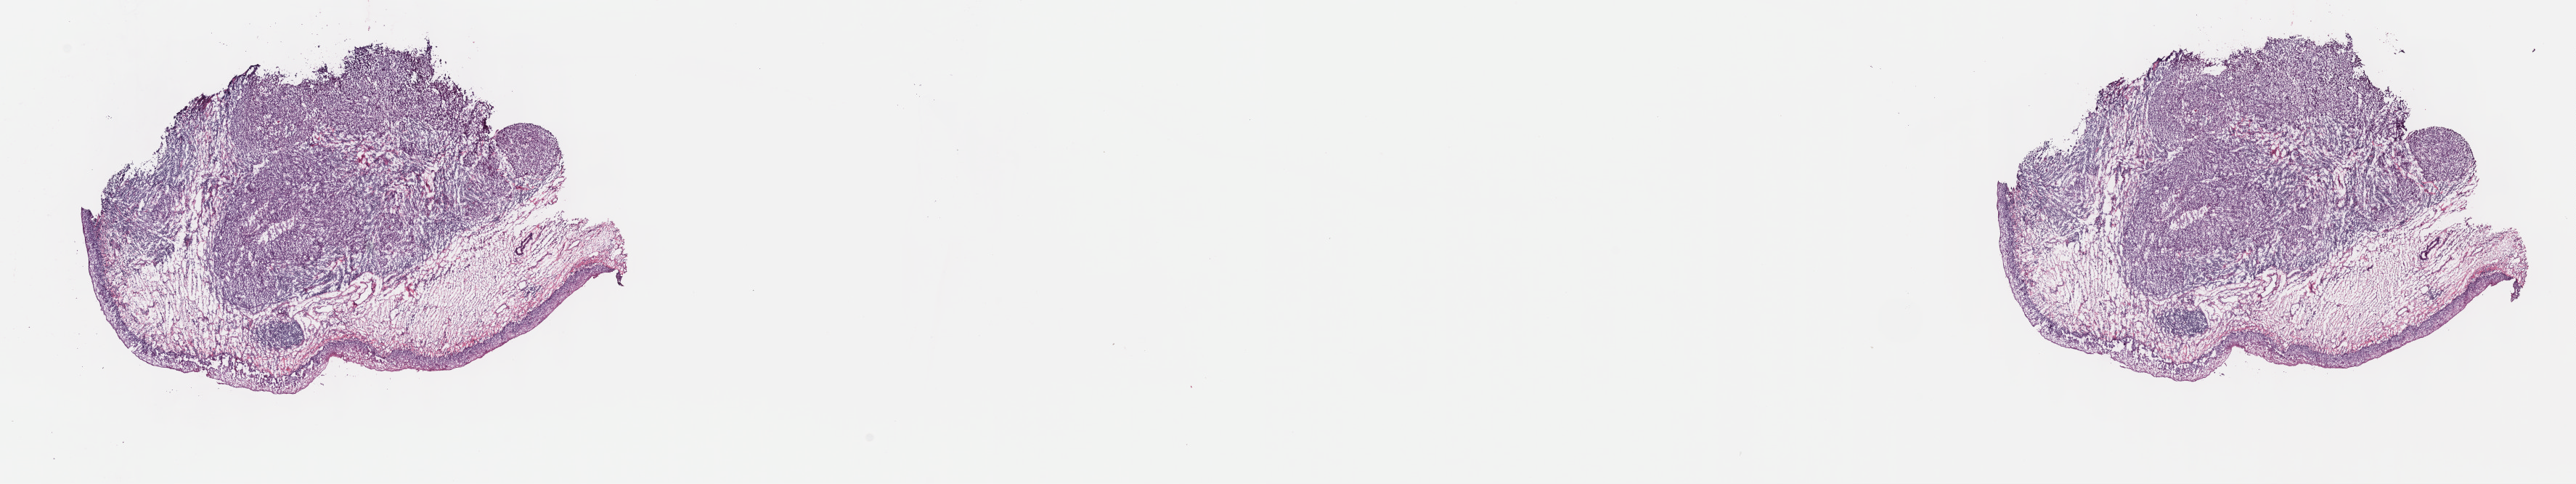
Whole-slide histology image, H&E, a low-resolution overview of the entire scanned area, about 28.7 x 5.4 mm (acquisition: 40x scan). Frozen section from the top of the tissue portion. Sample: primary tumour, head and neck. Patient: male, age at initial diagnosis 59 years. Histologic grade: G2 (moderately differentiated). Slide review estimates, as recorded: tumour cells 70%, tumour nuclei 70%, normal cells 30%, stromal cells 0%, necrosis 0%. Inflammatory infiltration, as recorded: lymphocyte infiltration 5%, monocyte infiltration 0%, neutrophil infiltration 0%.
AJCC pathologic stage: IVA. Histologic diagnosis: Squamous cell carcinoma, NOS (hypopharynx, NOS).